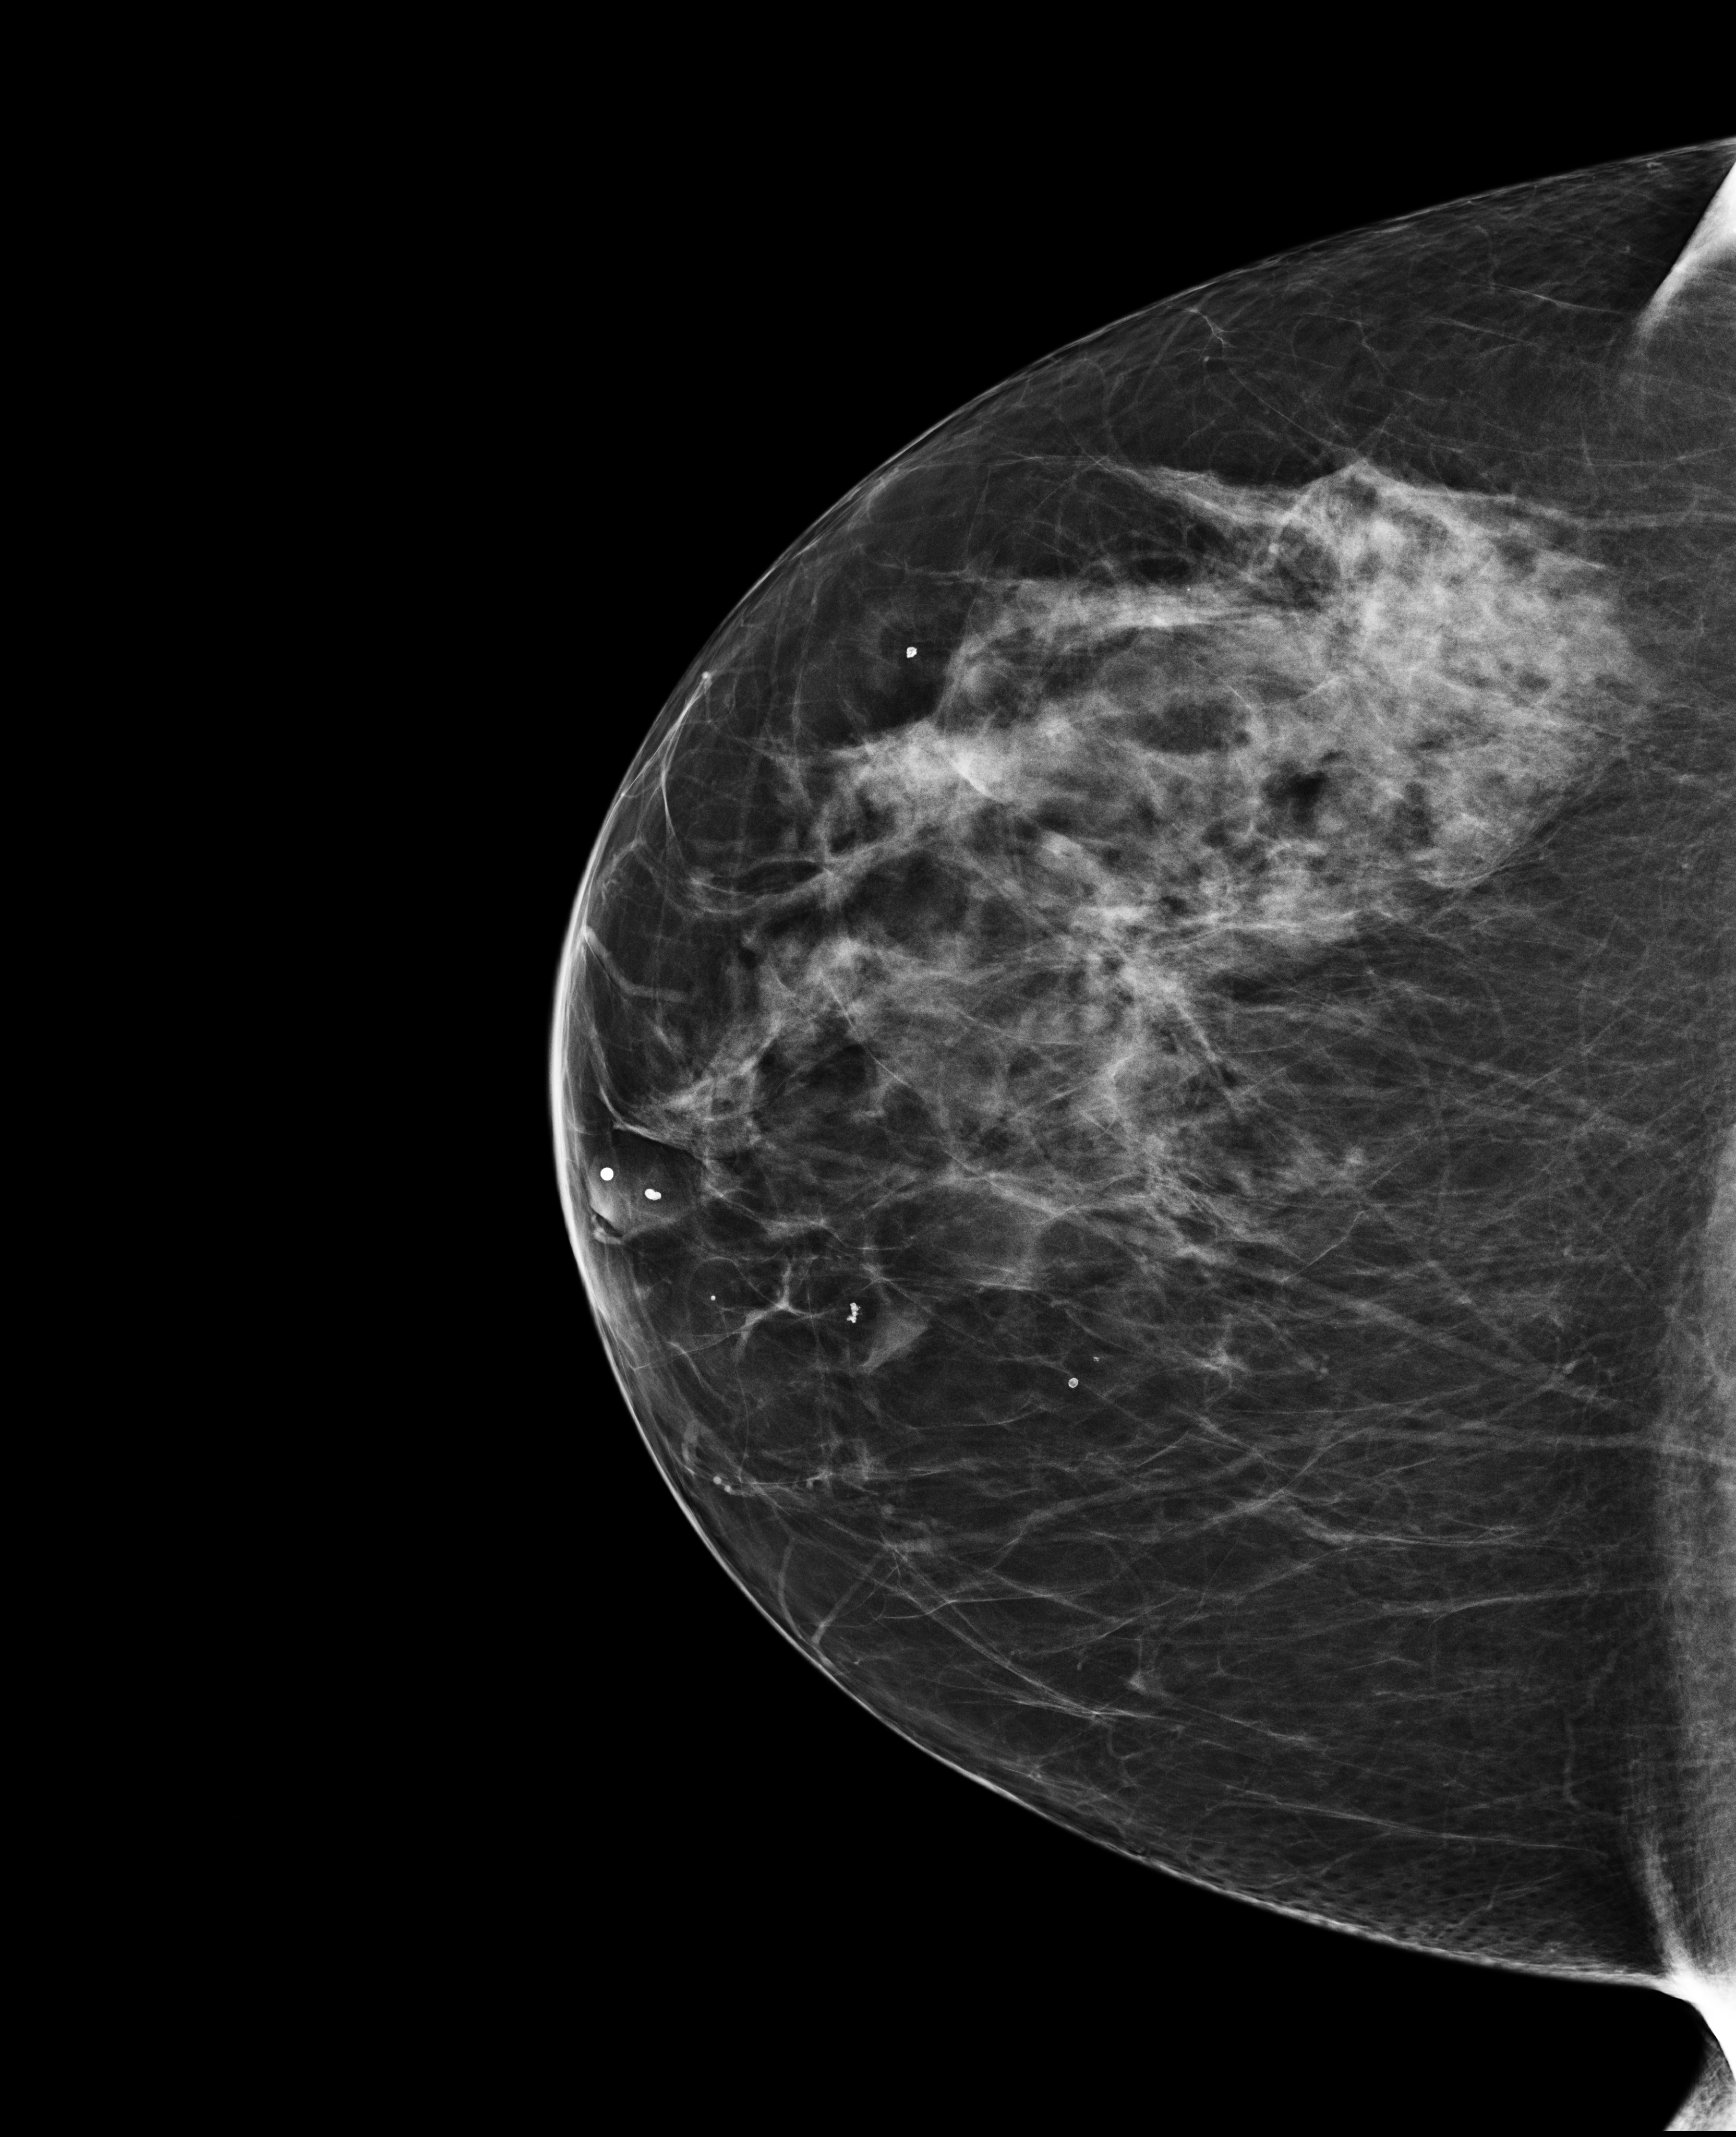
Digital mammogram (FFDM), right breast, CC view, screening examination. Patient: female, 60 years.
BI-RADS breast density category at the screening exam (both breasts, scale 1–4): 3. Final BI-RADS assessment for this screening round (tomosynthesis exam, both breasts): category 1. Recall: no recall after this screen.